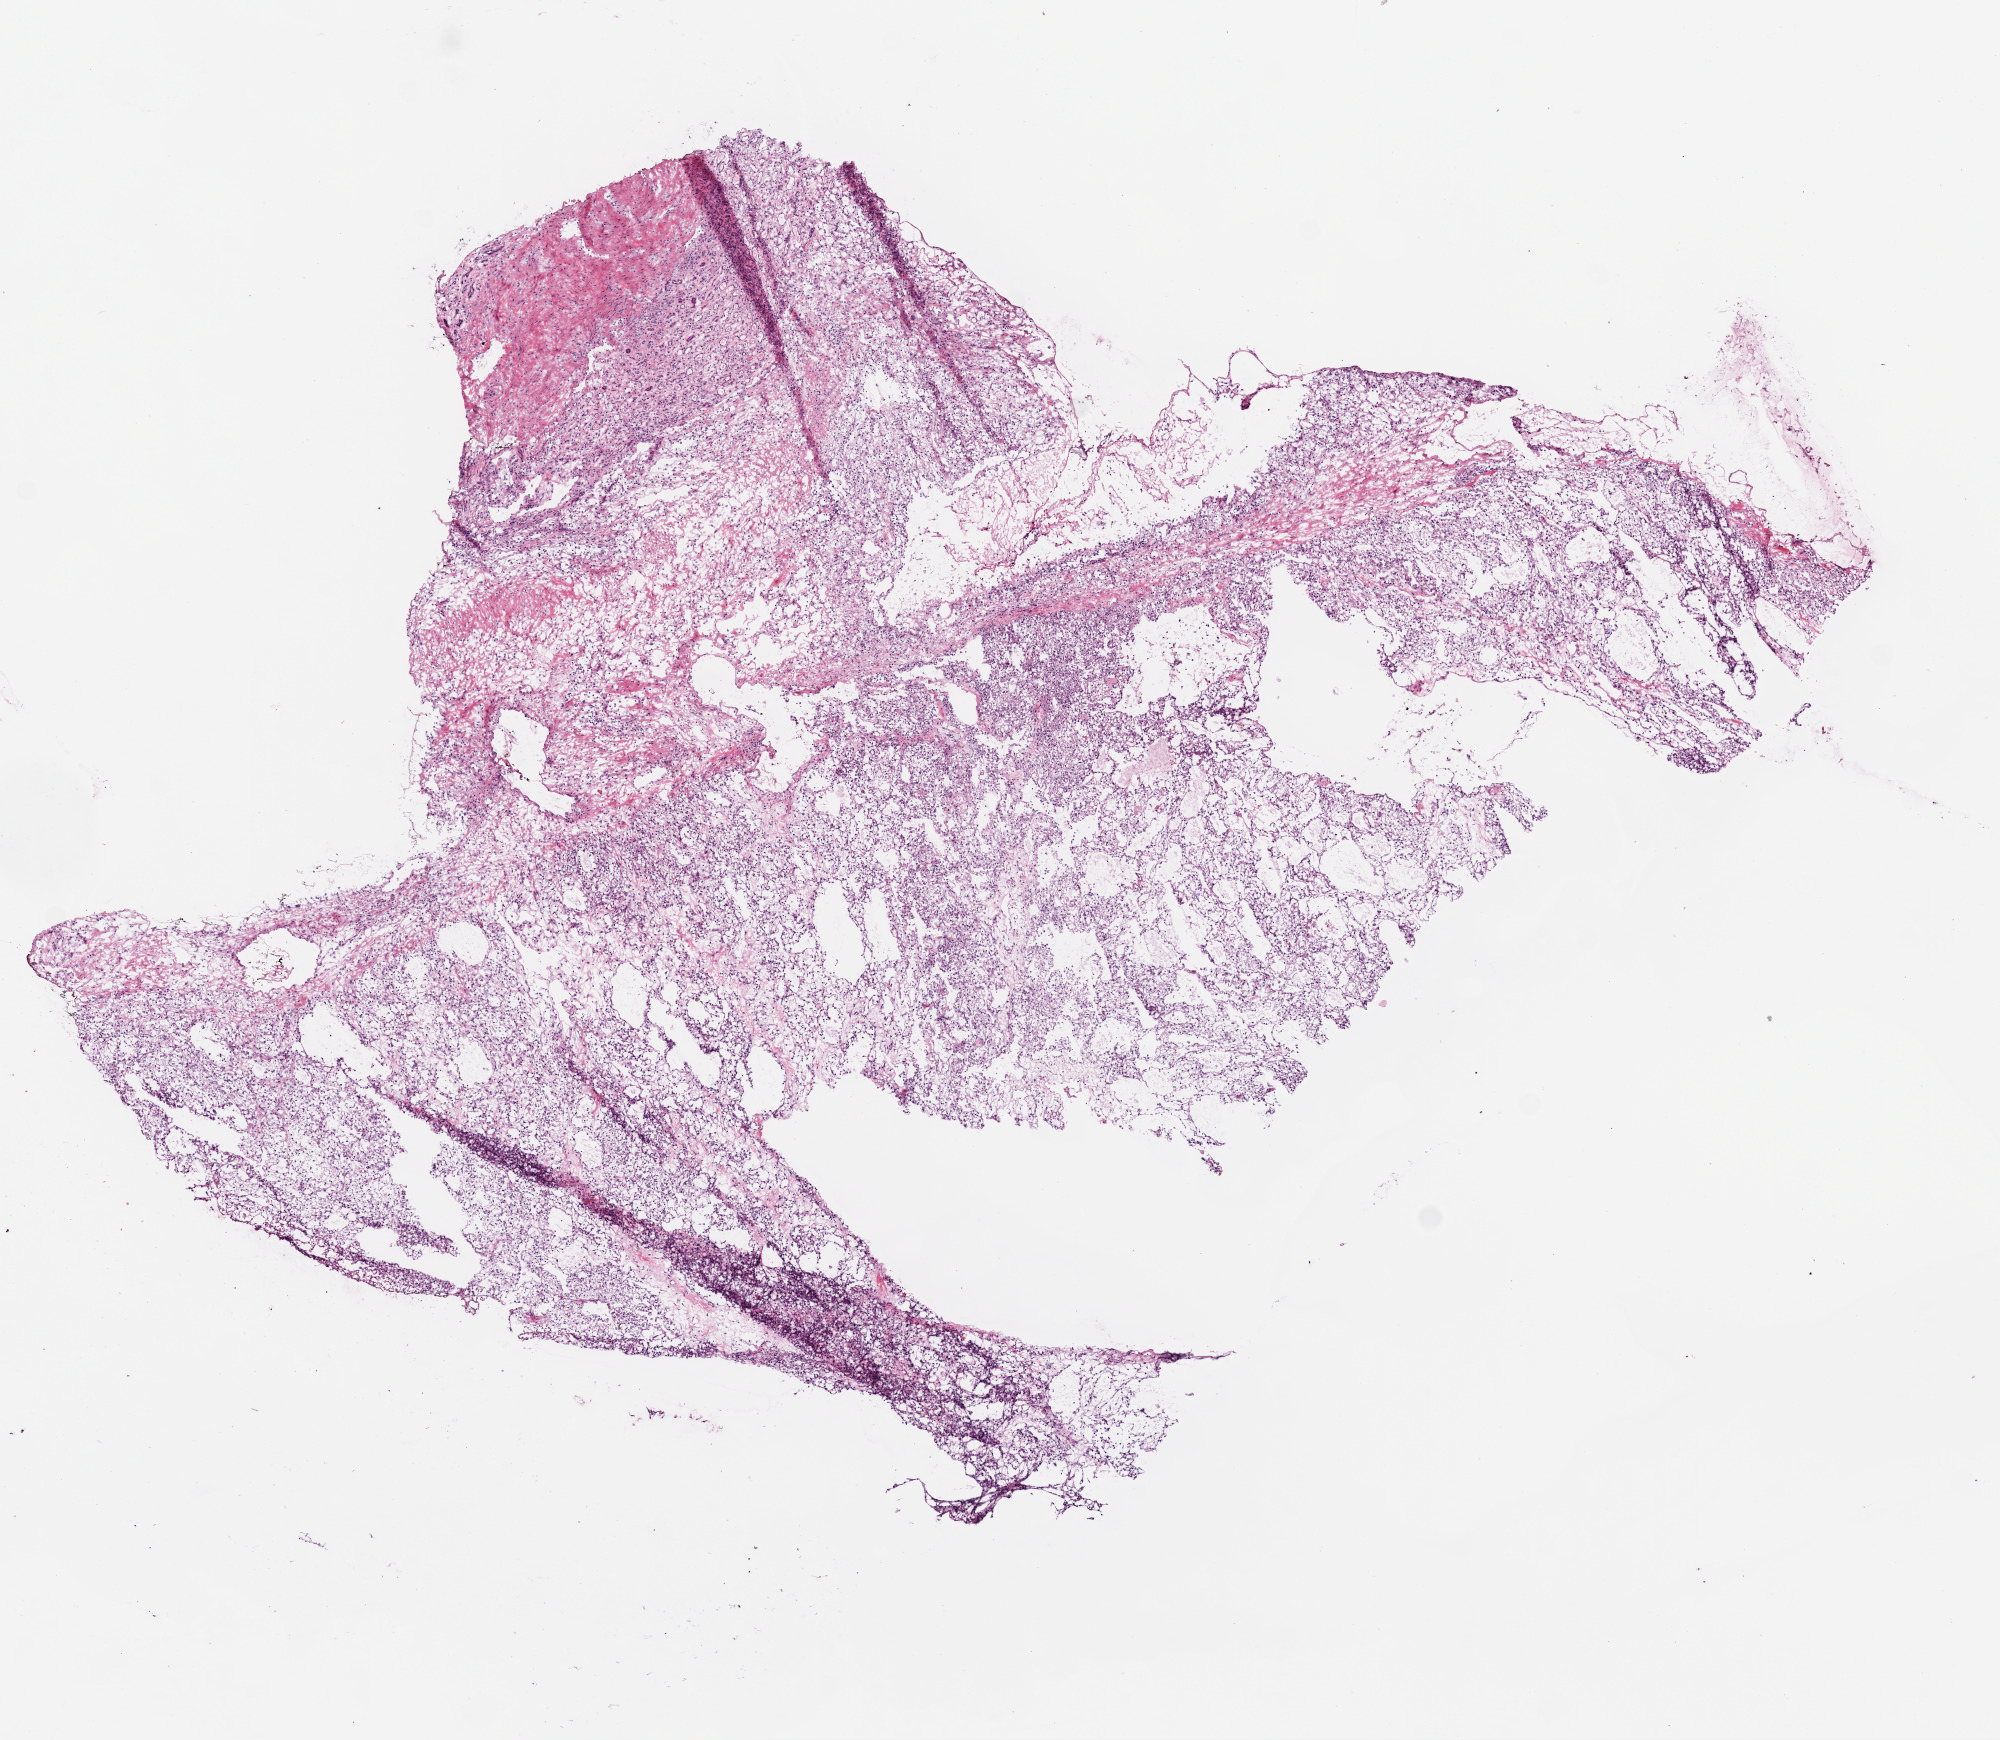
Whole-slide histology image, H&E-stained, whole scanned area (about 8.0 x 7.0 mm, from a 20x scan) shown as a low-resolution overview. Frozen section. Sample: primary tumour, kidney. Patient: female, age at initial diagnosis 54 years. Histologic grade: G3 (poorly differentiated). Slide review estimates, as recorded: tumour cells 65%, tumour nuclei 80%, normal cells 15%, stromal cells 20%, necrosis 0%.
• AJCC pathologic stage: I
• histologic diagnosis: Clear cell adenocarcinoma, NOS